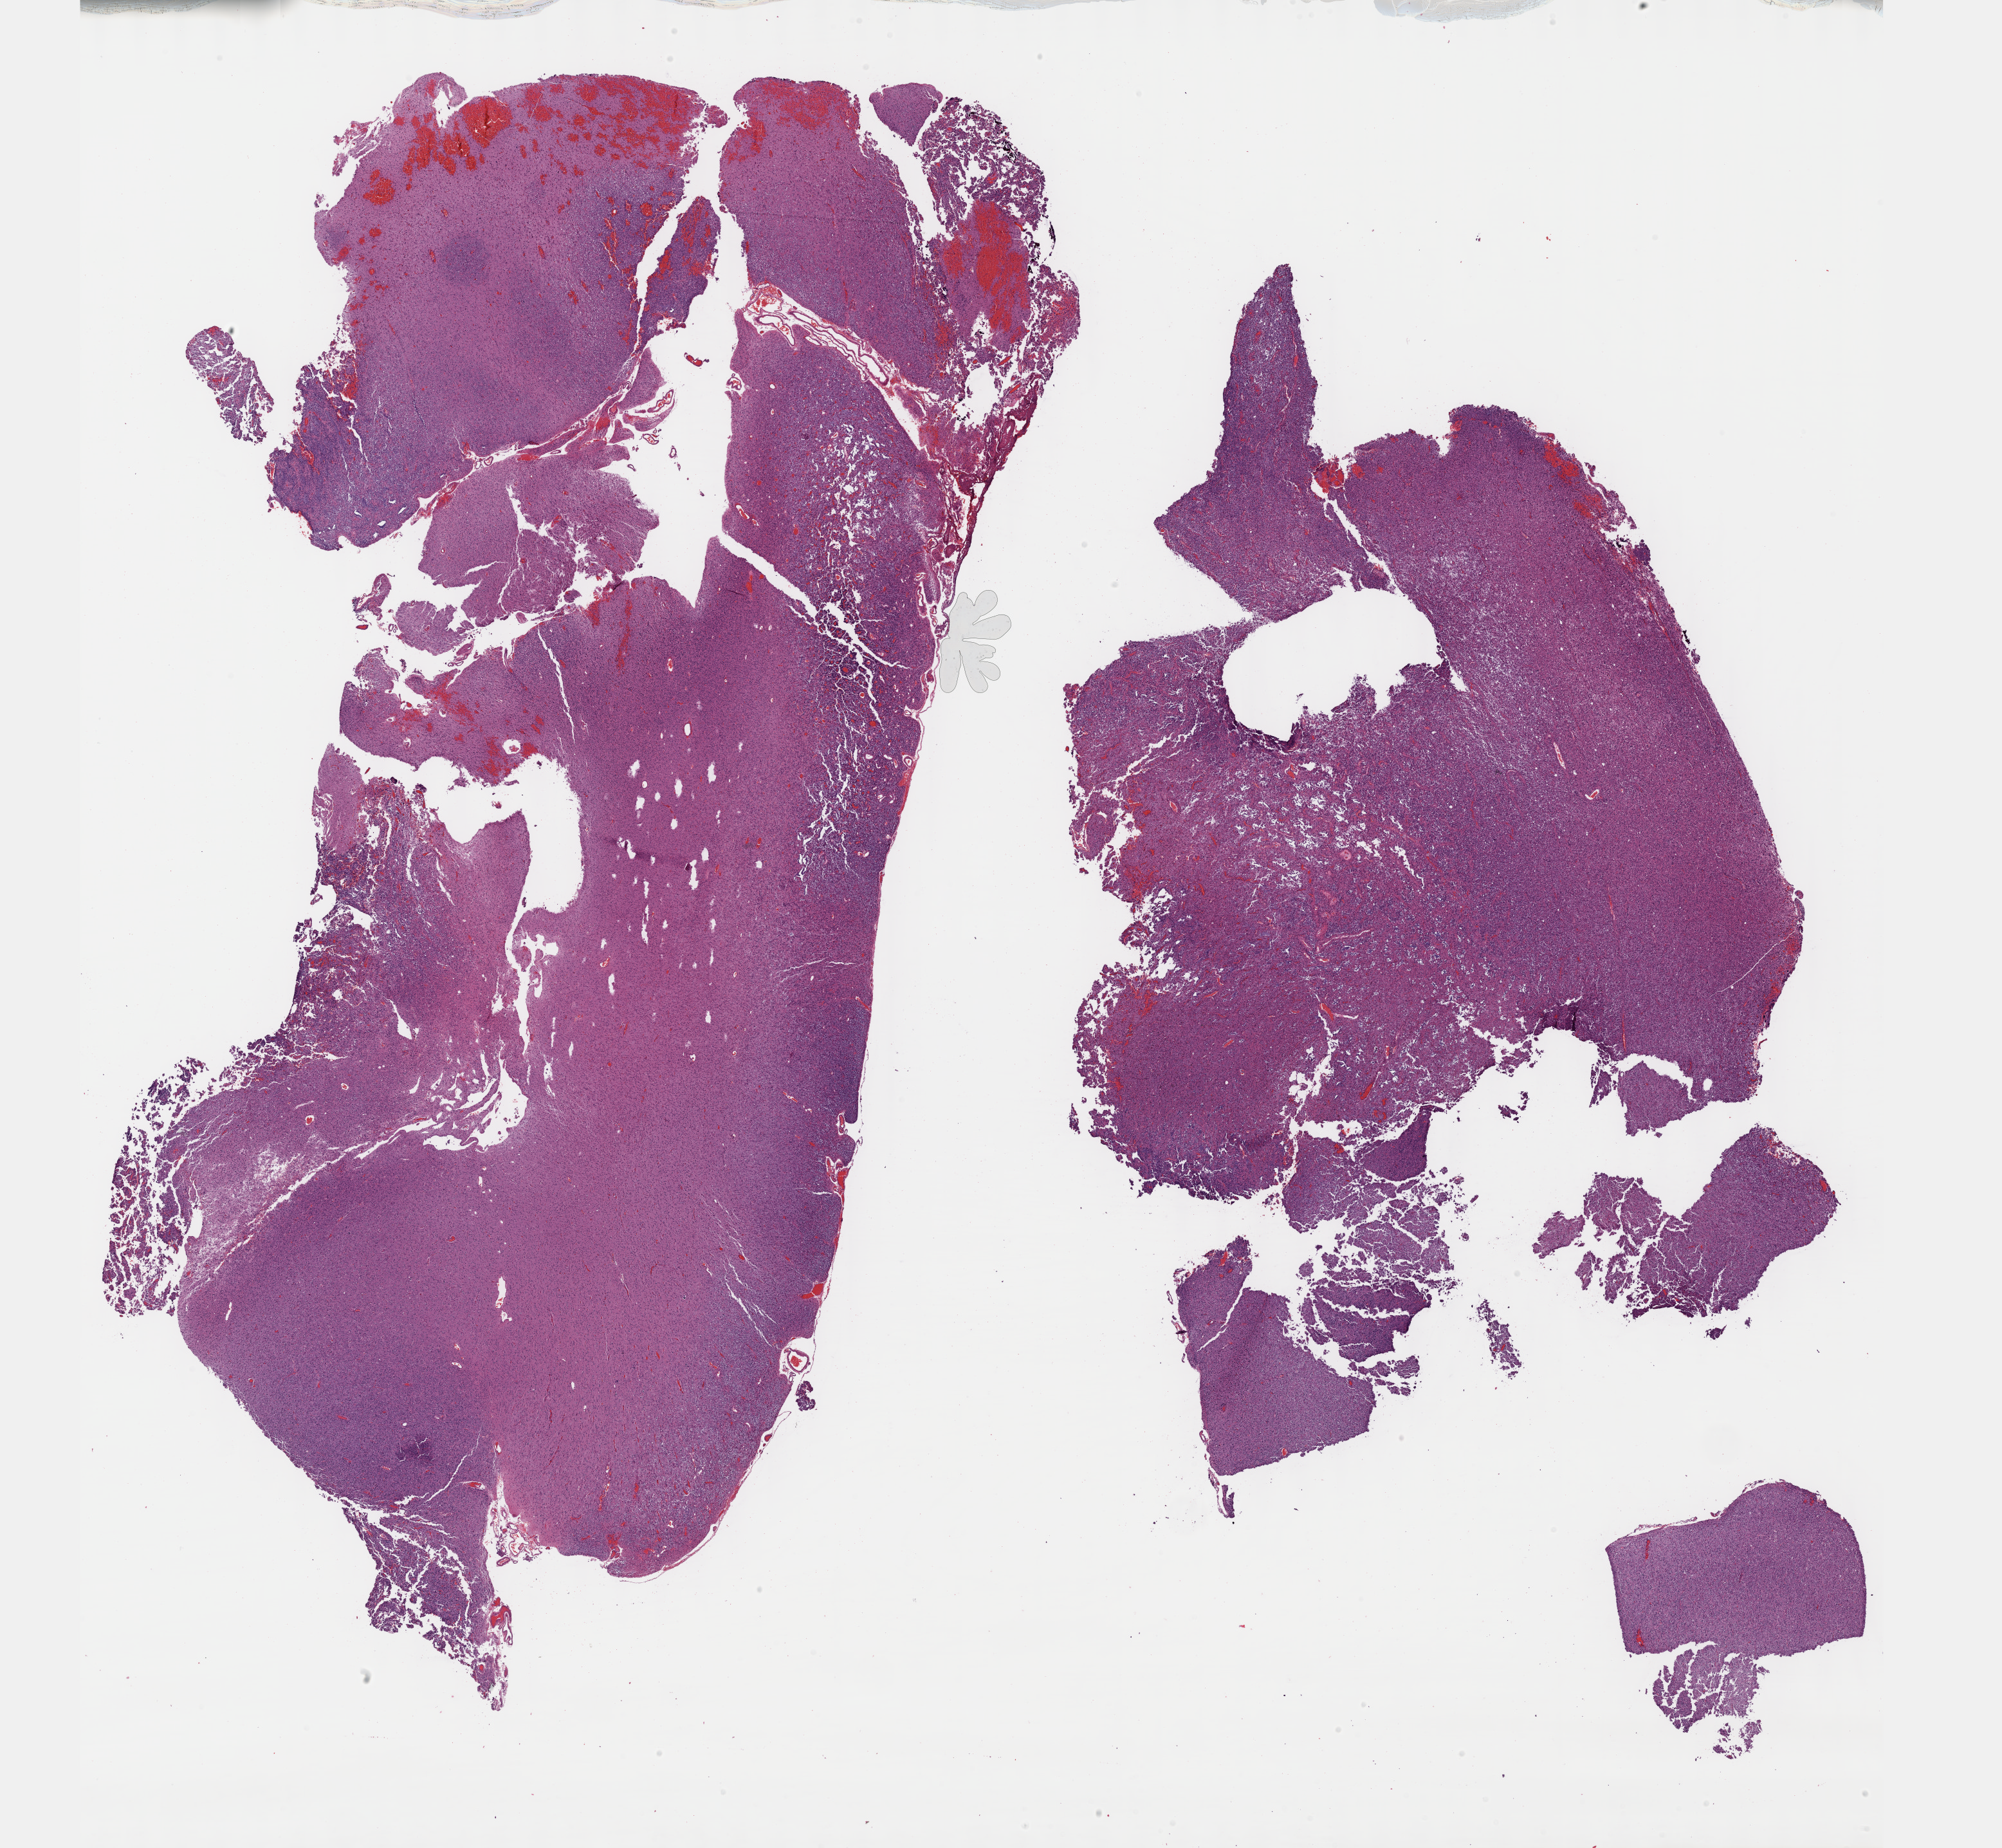
Hematoxylin and eosin (H&E) stained whole-slide image — shown as a low-resolution overview of the whole scanned area (about 25.1 x 23.2 mm, acquisition: 40x scan); FFPE section; primary tumour sample from the brain. Male patient; age at initial diagnosis 59 years. Histologic grade: G3 (poorly differentiated).
• laterality: left
• pathologic diagnosis: Oligodendroglioma, anaplastic (cerebrum)